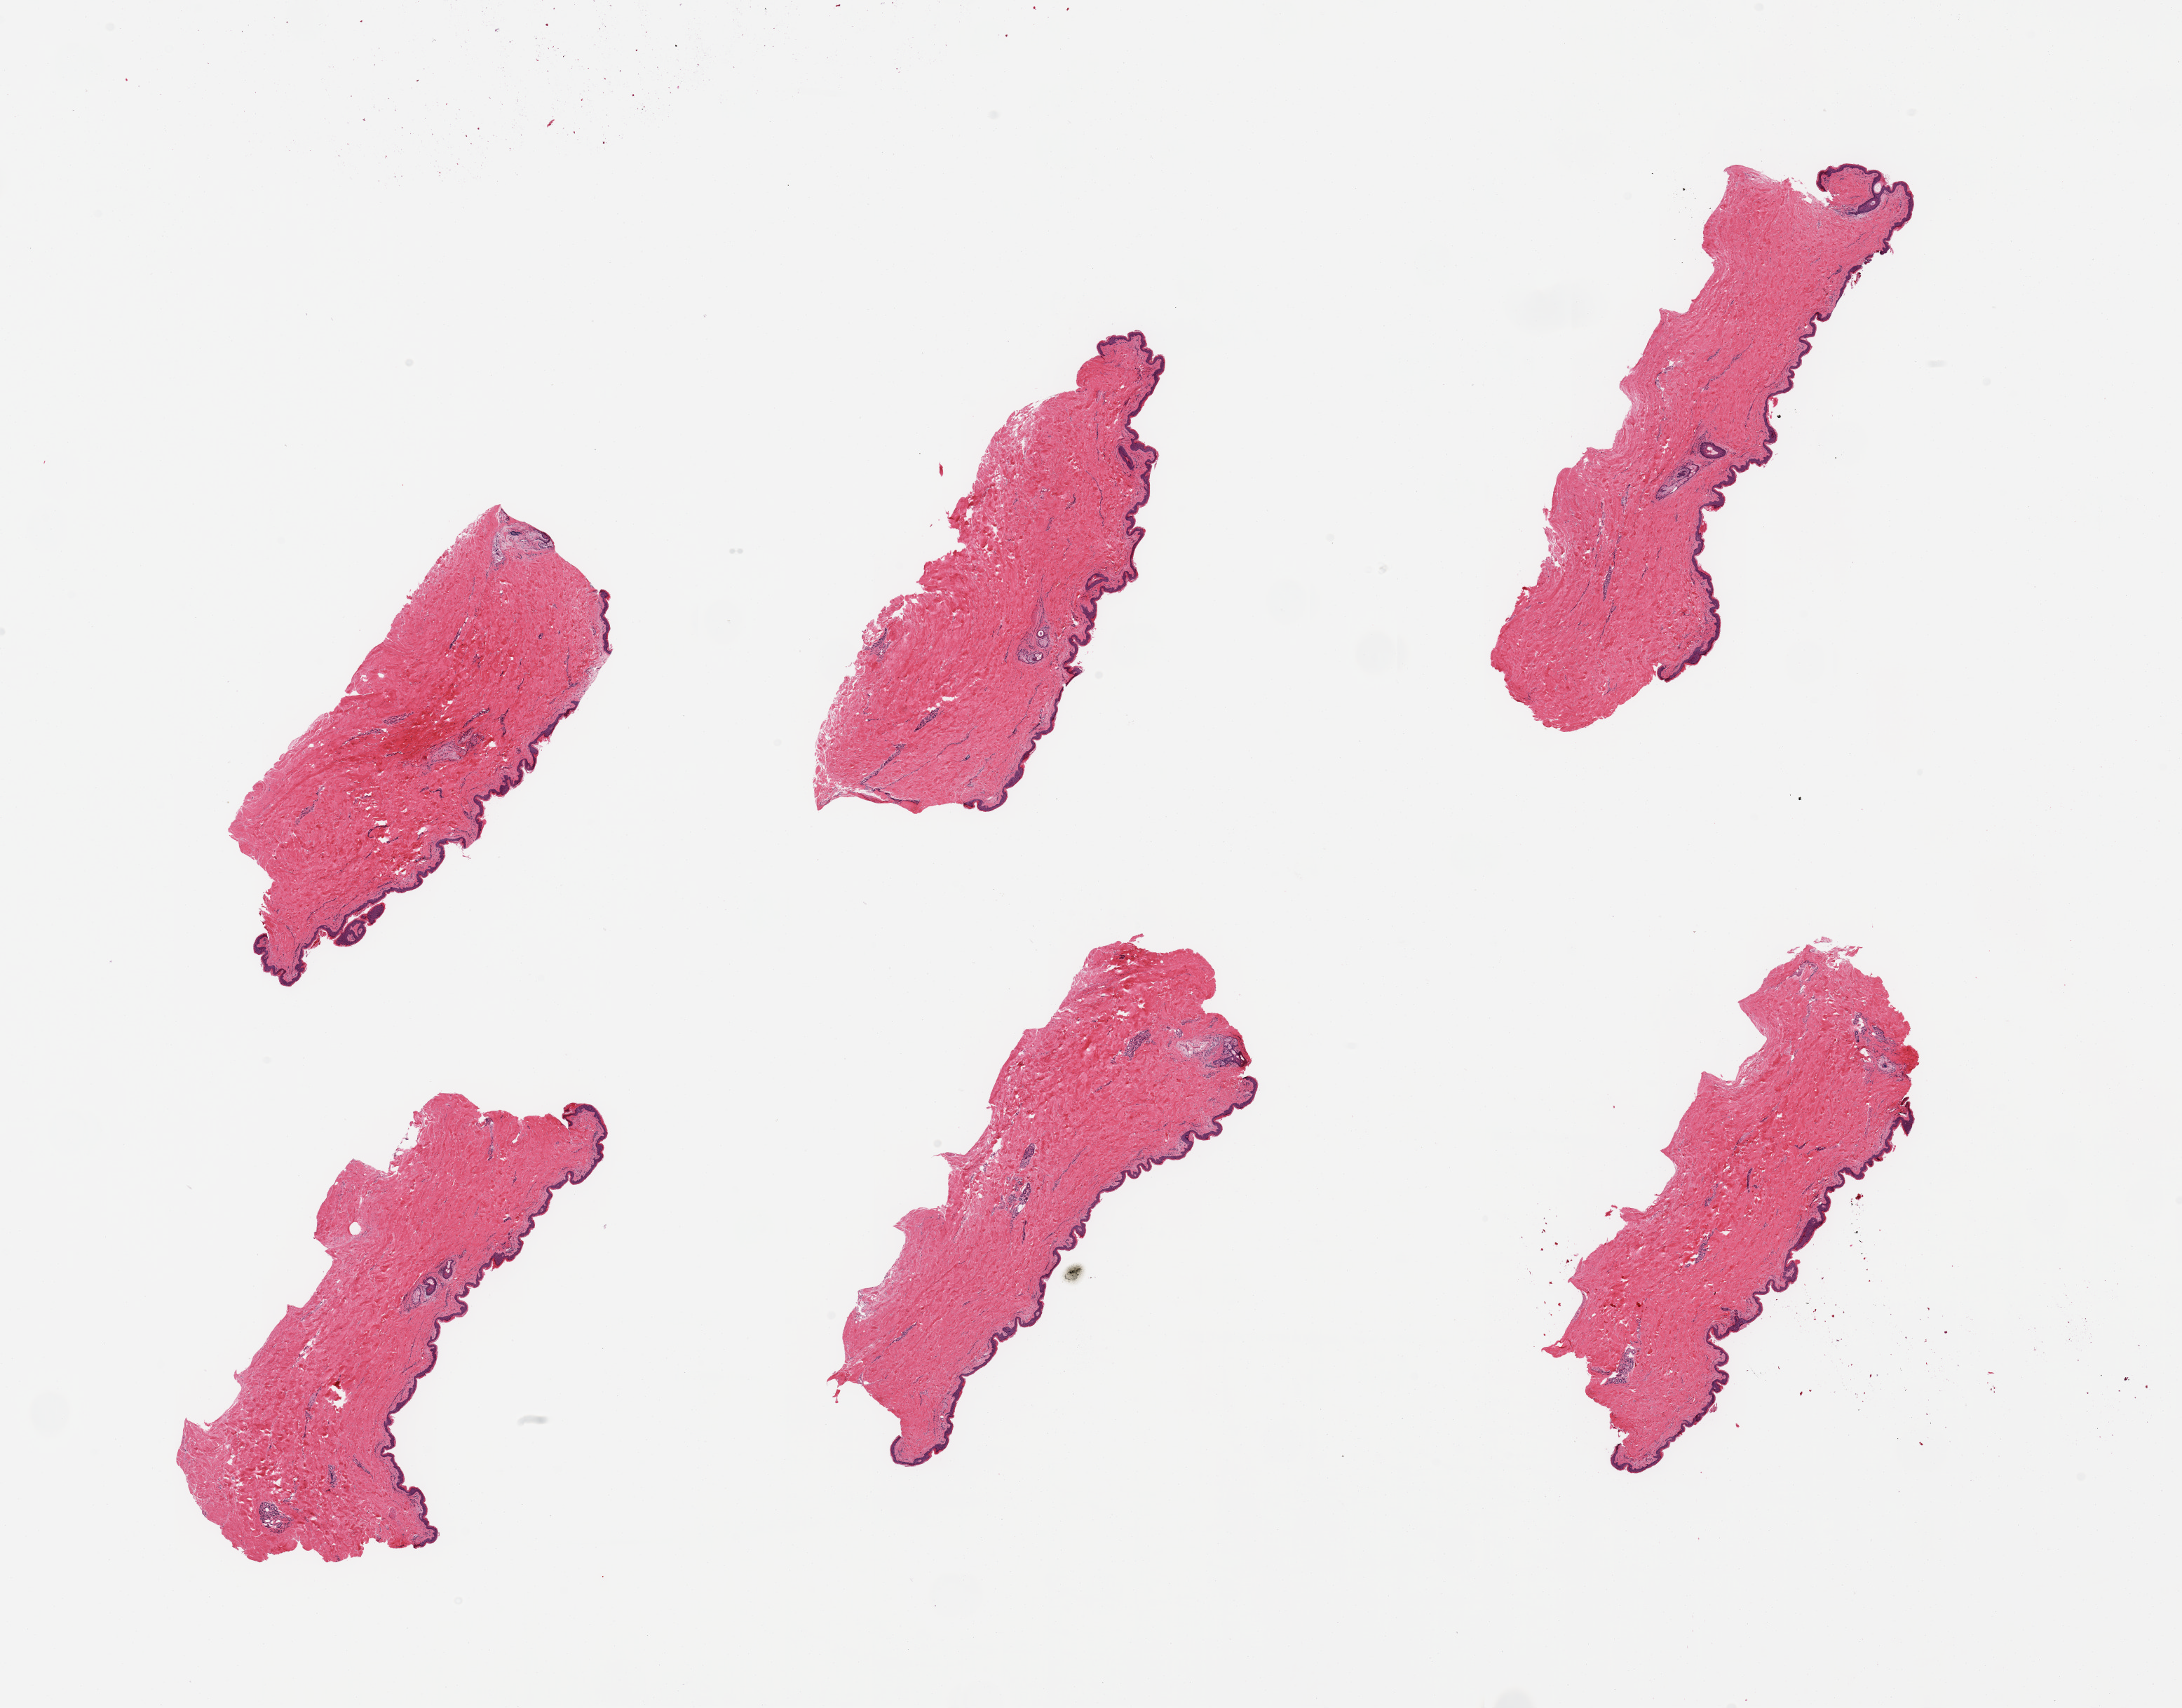
Whole-slide image, hematoxylin and eosin (H&E) stain, low-resolution overview of the scanned area, about 24.6 x 19.3 mm (slide scanned at 20x). PAXgene-fixed paraffin-embedded (PFPE) section. Sampled site (target tissue): skin of suprapubic region. Tissue donor sample. Male donor.
Reviewer comment on this tissue sample: 6 pieces; well dissected skin; <1% dermal fat.